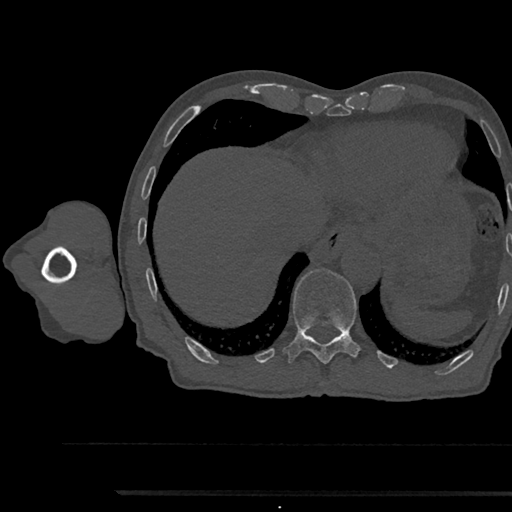
CT including the spine, one axial slice; position 788 of 797 along the scan axis; reconstruction kernel Br40s/3; 120 kVp; bone window (W 1800 / L 400 HU); 512 × 512 image matrix. Patient: male, 79 years. From the clinical record (not read from this slice): primary cancer: prostate.
Outlined on this slice (semi-automatically segmented with operator editing):
- T11 vertebra: box from (x=284, y=268) to (x=360, y=364) px